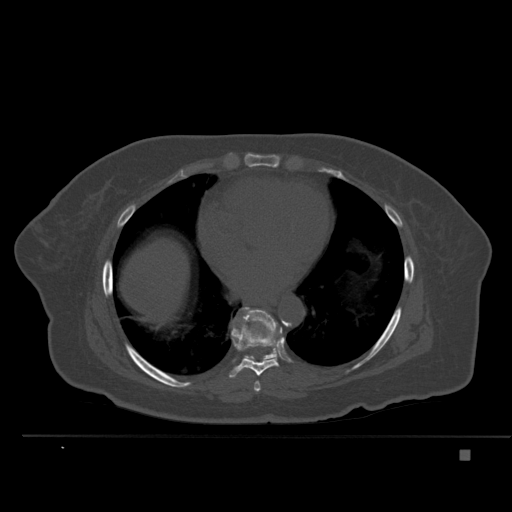
CT including the spine, one axial slice; bone window (W 1800 / L 400 HU); 512 × 512 image matrix. Patient: female, 74 years. Case-level facts recorded for this patient, not image findings: primary cancer: colon.
Annotated regions visible in this slice (semi-automatically segmented with operator editing):
- T7 vertebra: bounding box <254,382,261,392> (left, top, right, bottom; pixels)
- T8 vertebra: <229,324,282,378>
- T9 vertebra: <233,307,279,363>